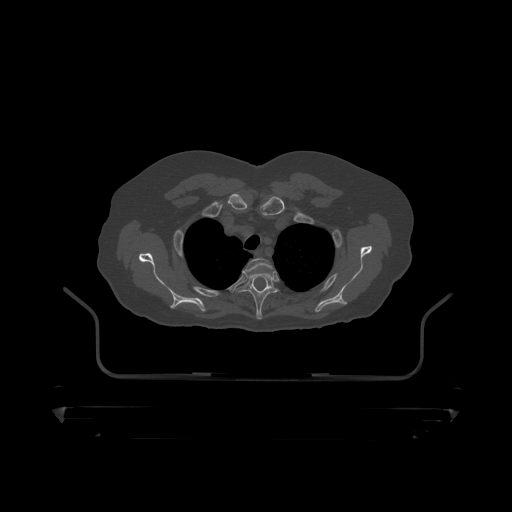
CT including the spine, one axial slice. Bone window (W 1800 / L 400 HU). 1.25 mm slice thickness. 512 × 512 image matrix, field of view 650 × 650 mm. Male patient, age 60 years. From the clinical record (not read from this slice): primary cancer: prostate.
Annotated regions visible in this slice (semi-automatically segmented with operator editing):
- T2 vertebra: bounding box (x1, y1, x2, y2) in pixels: (246, 258, 272, 272)
- T3 vertebra: (237, 266, 281, 319)